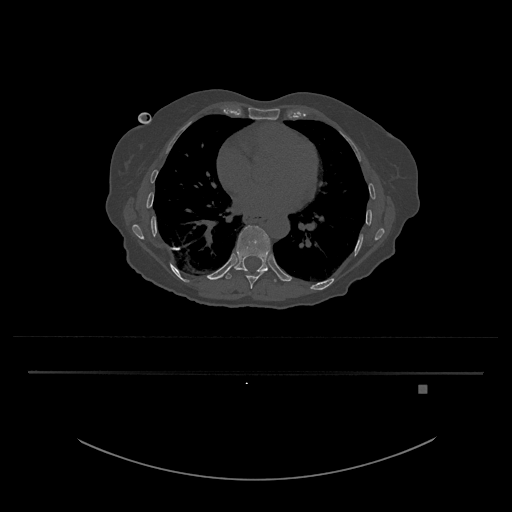
CT including the spine, one axial slice. Position 735 of 797 along the scan axis. Bone window (W 1800 / L 400 HU). 0.5 mm slice thickness. 512 × 512 image matrix, field of view 500 × 500 mm. Patient: female, 57 years. Case-level facts recorded for this patient, not image findings: primary cancer: cervical.
Outlined on this slice (semi-automatic segmentation, software-assisted and operator-edited):
- T10 vertebra: box from (x=224, y=225) to (x=277, y=282) px
- T9 vertebra: (x=247, y=275)–(x=259, y=289)